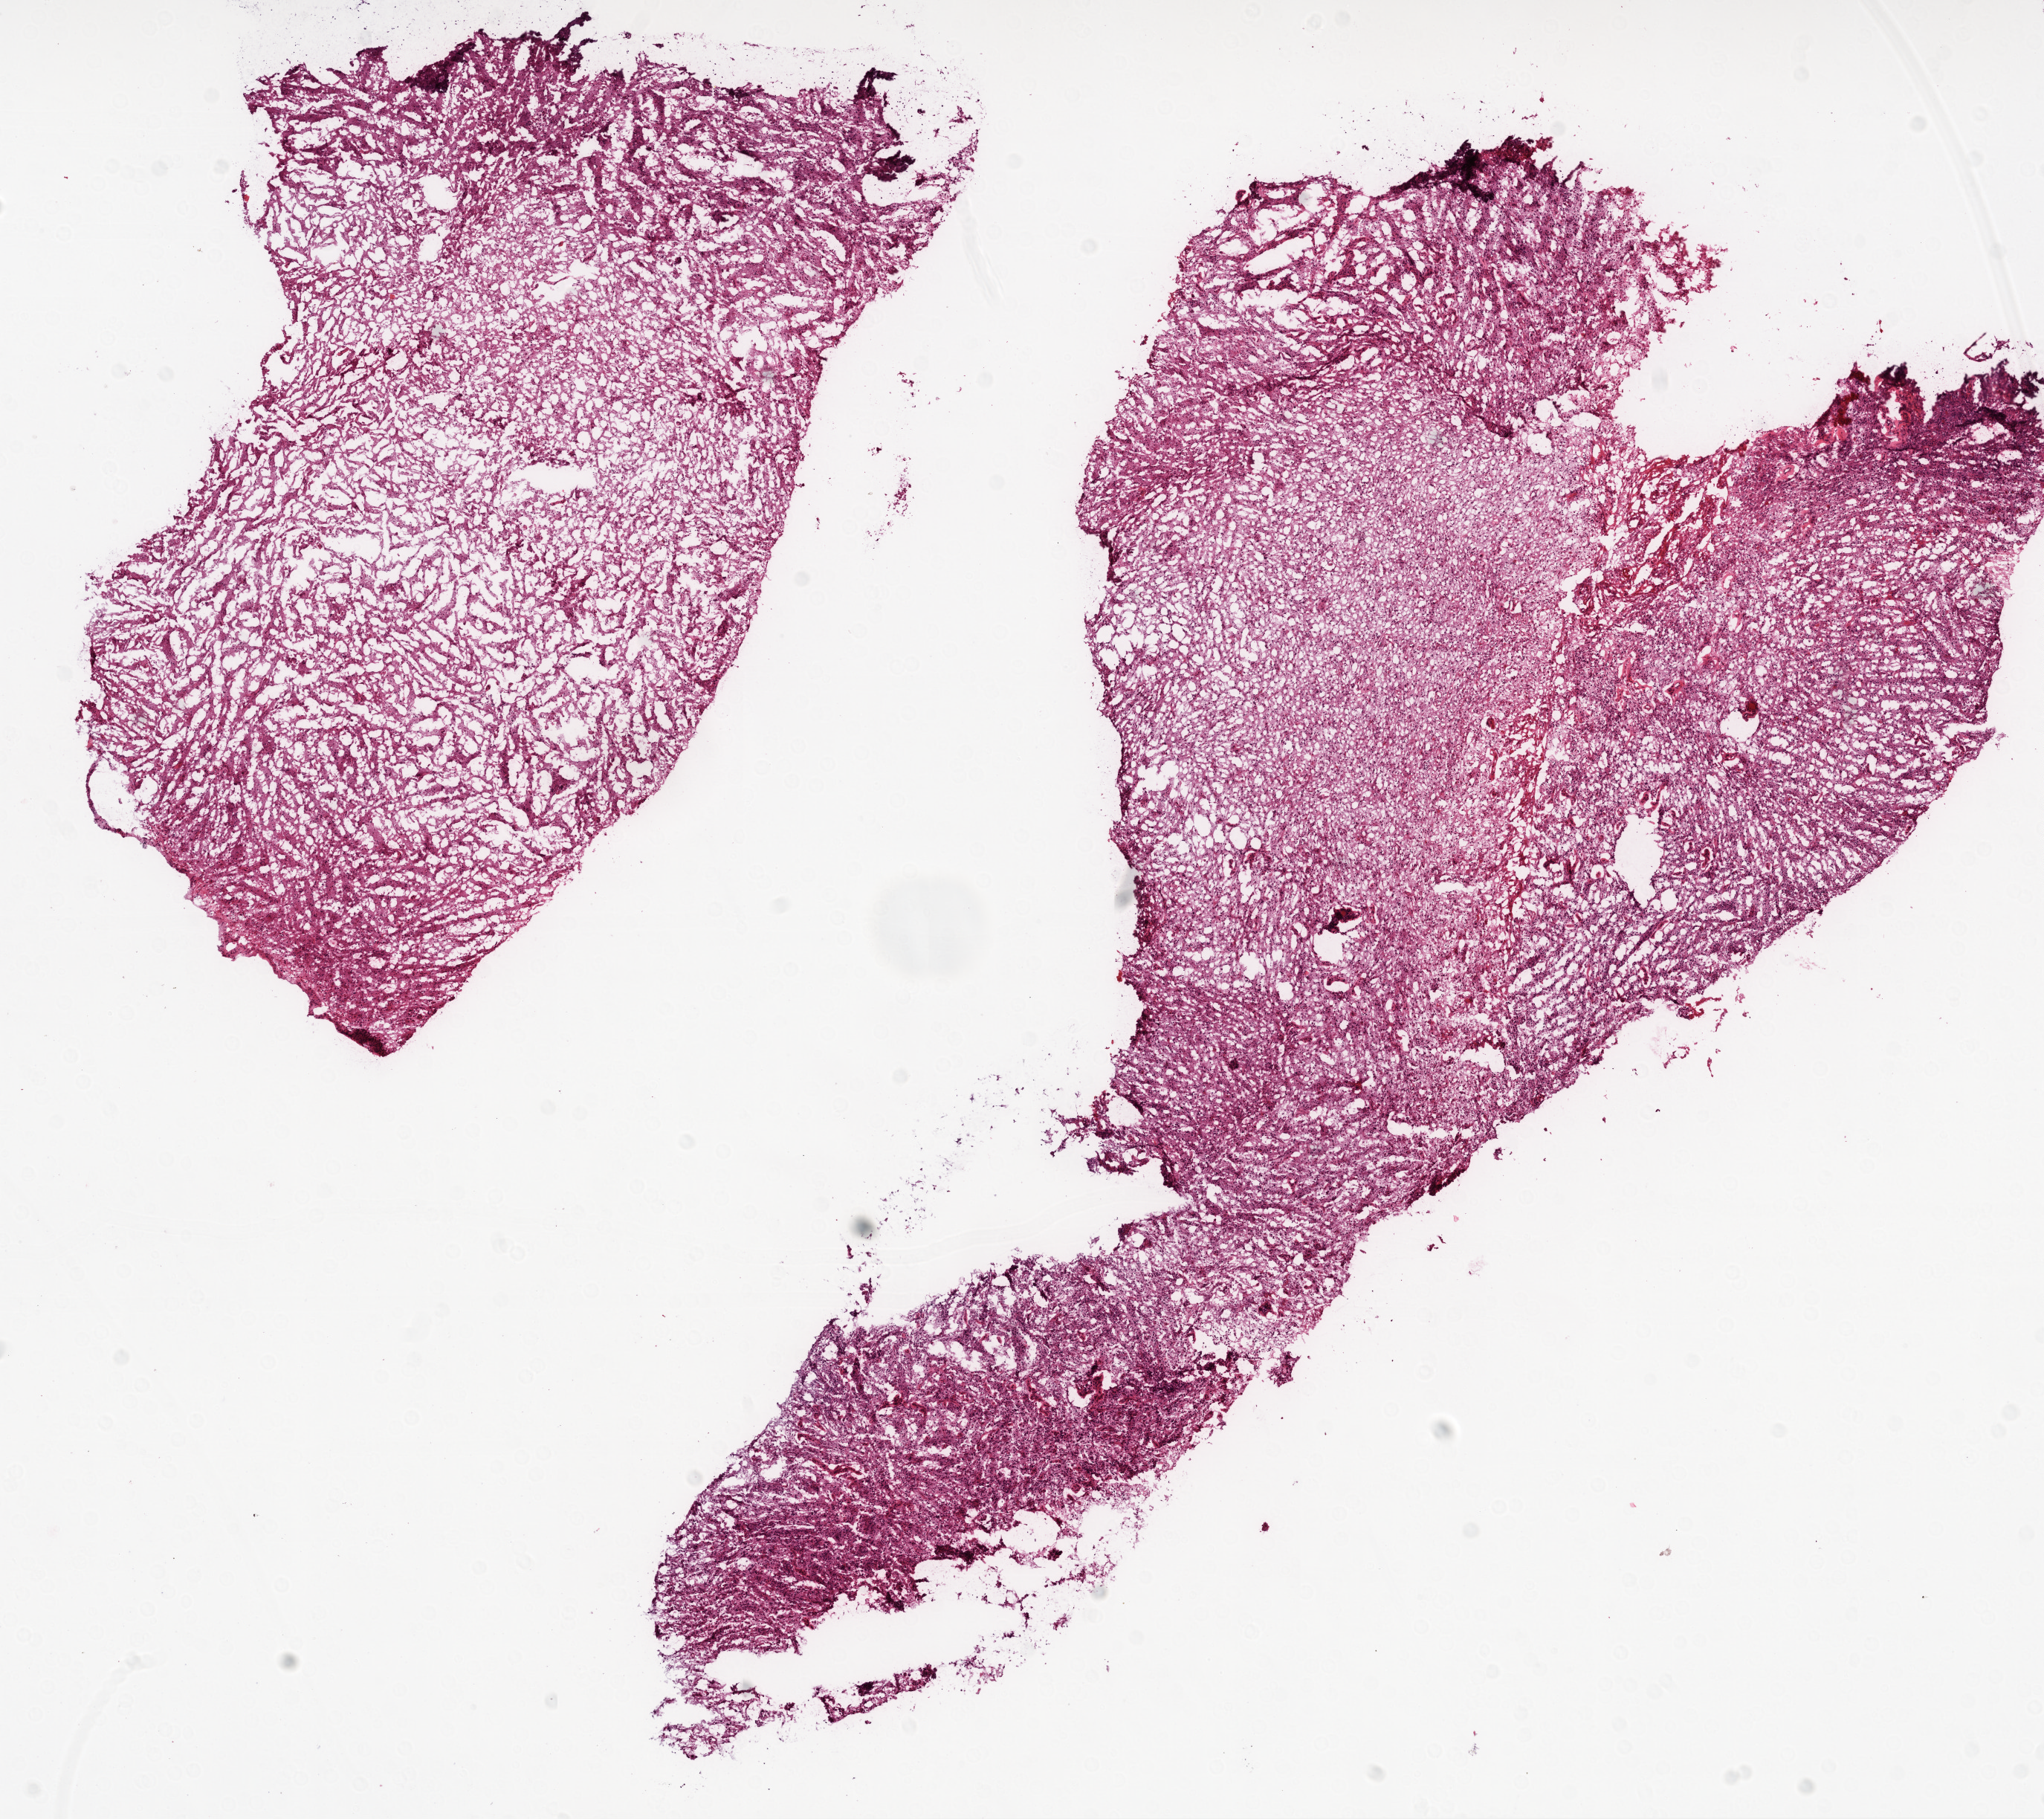
Whole-slide histology image, Hematoxylin and eosin (H&E) stained — whole scanned area (about 11.0 x 9.8 mm, slide scanned at 20x) shown as a low-resolution overview, frozen section from the top of the tissue portion, primary tumour sample from the brain. Male, age 55 years at initial diagnosis. Composition of this section per pathologist review: tumour cells 95%, tumour nuclei 100%, normal cells 0%, stromal cells 0%, necrosis 5%.
Histologic diagnosis: Glioblastoma.